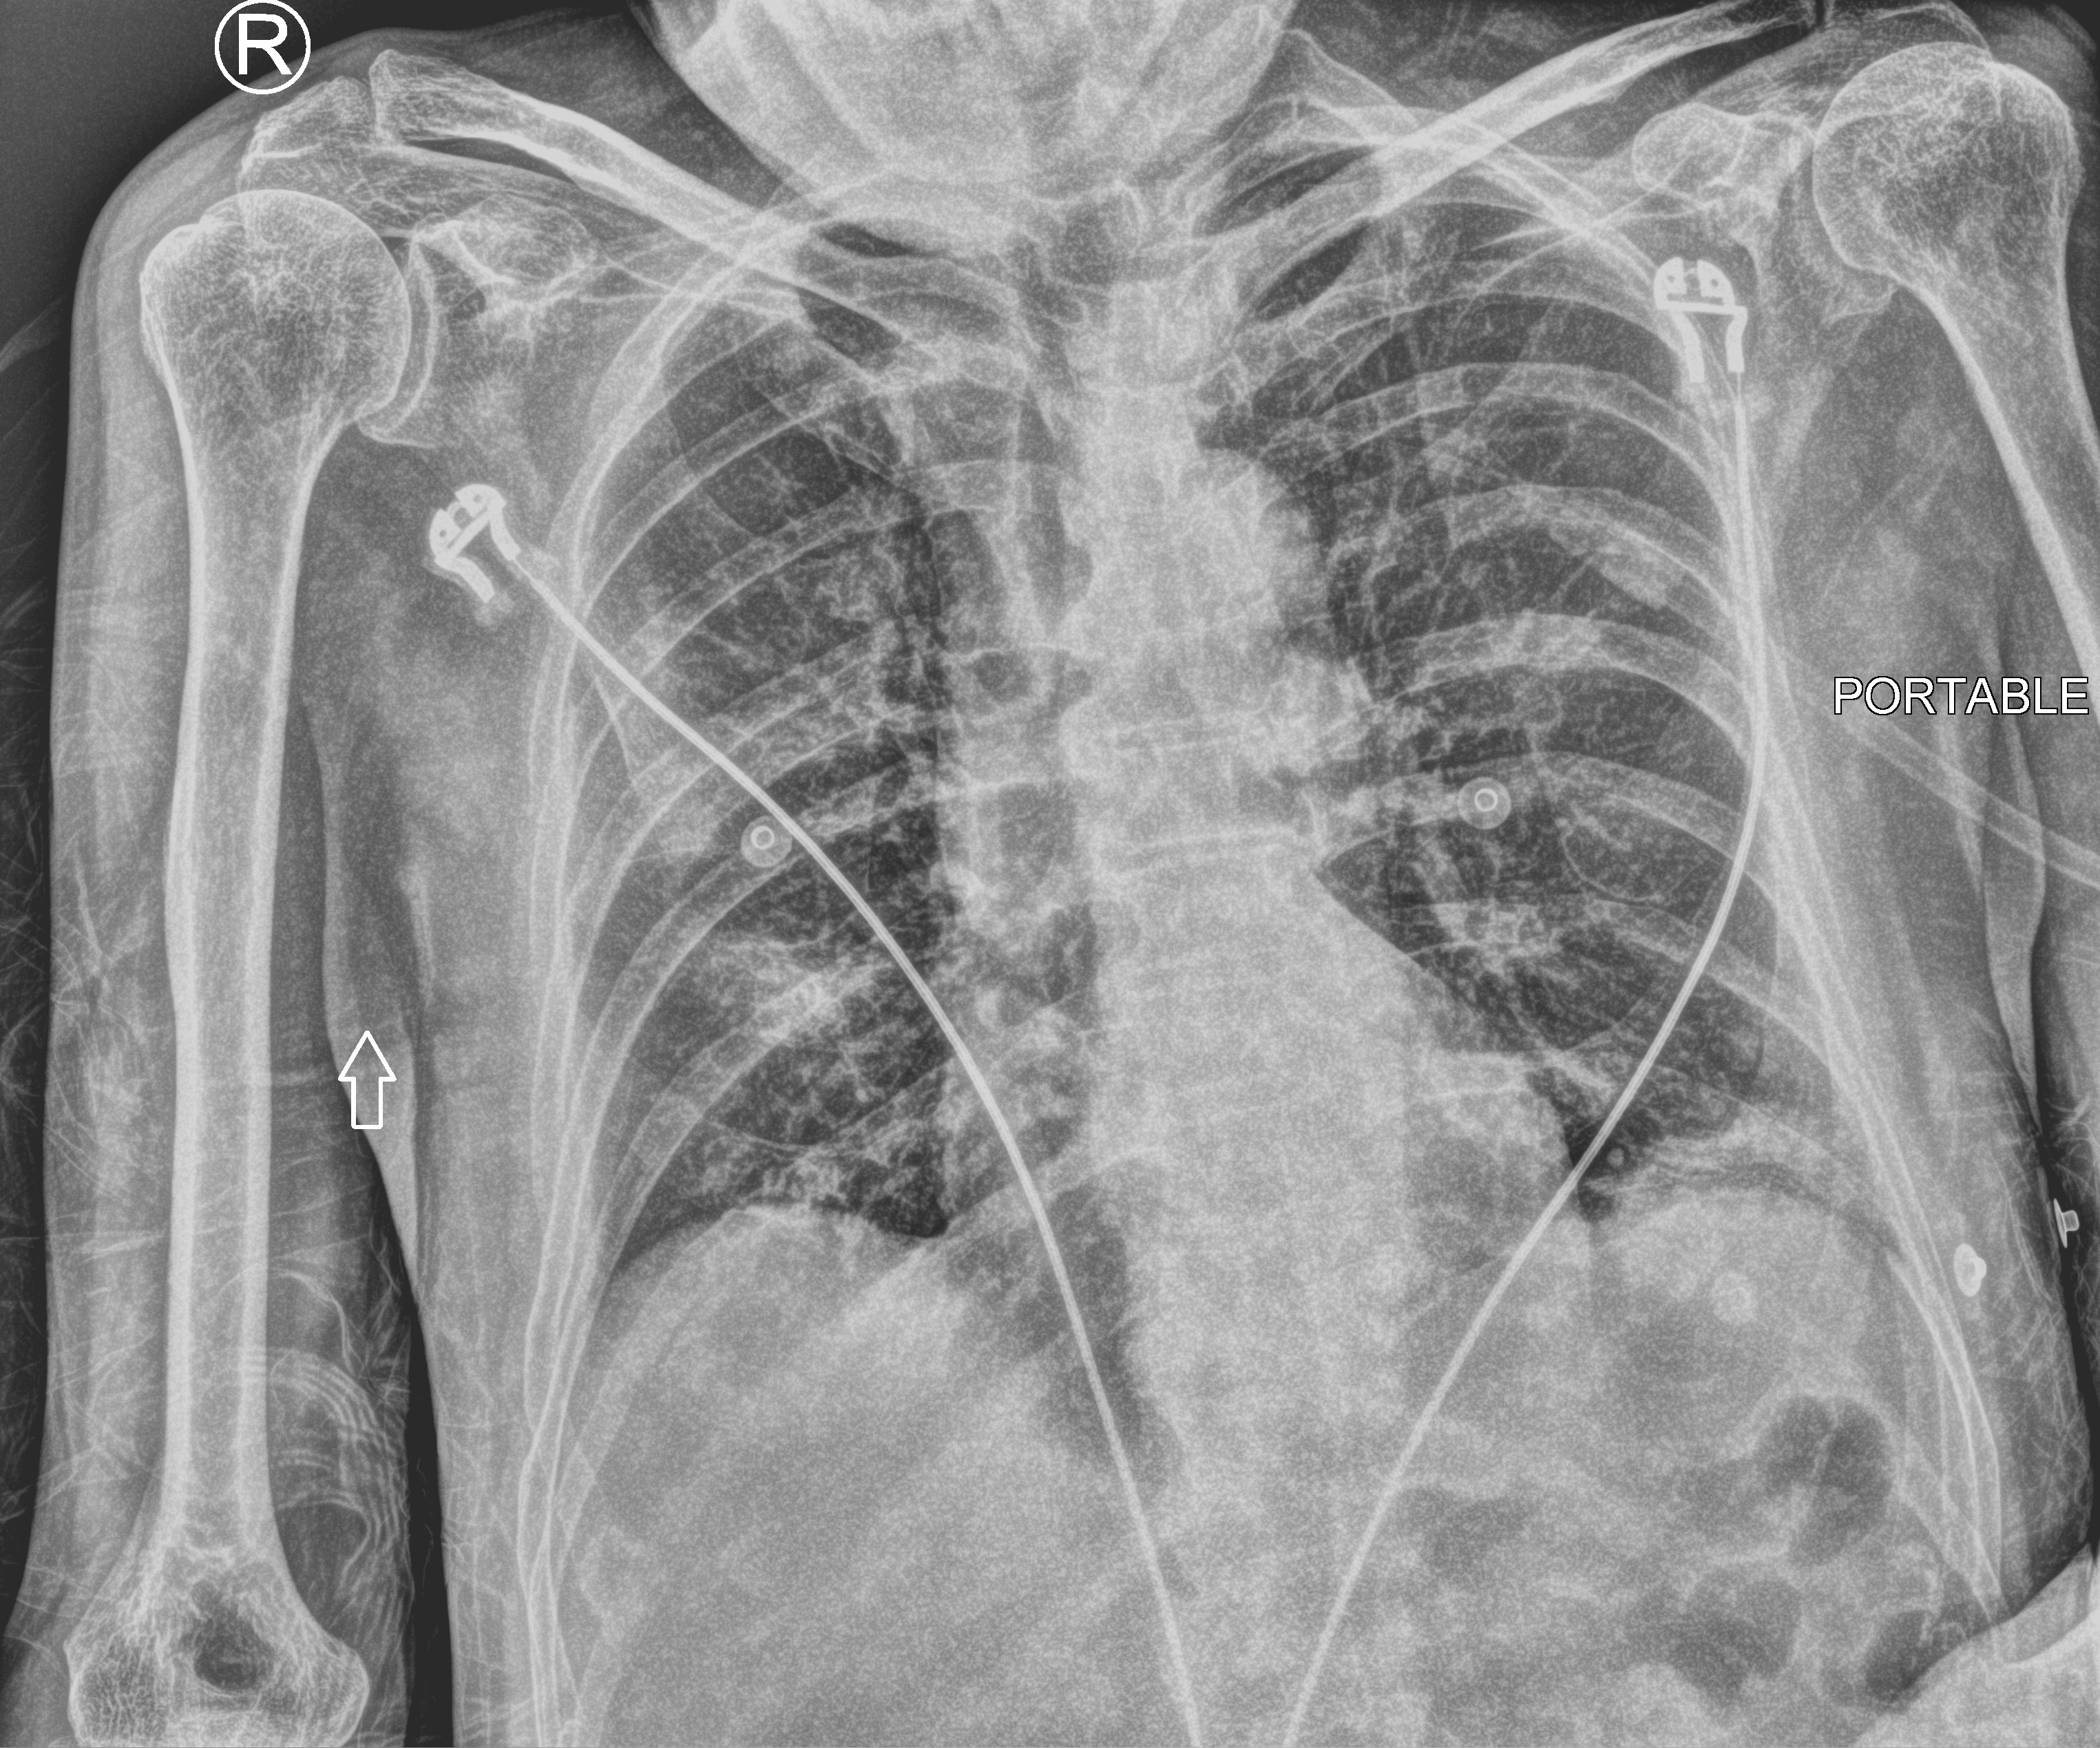
Portable chest radiograph; anteroposterior (AP) projection. Male patient hospitalised with COVID-19, age 60–74 years.
Admission-level facts for this patient (not findings on this image; timing relative to this image not recorded): mechanically ventilated during this hospital stay: yes; COPD (admission record): no.